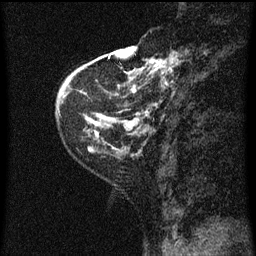
Breast MRI (dynamic contrast-enhanced), one sagittal slice. Slice 15 of 60 in the series (ordered by position). Dynamic contrast-enhanced series, image 2 of 3 at this slice position (ordered by acquisition). 1.5 T. TE 4.2 ms, TR 8 ms. 2 mm slice thickness. 256 × 256 image matrix, field of view 180 × 180 mm. Female patient, age 48 years.
Structures marked on this image (semi-automatic segmentation, software-assisted and operator-edited):
- analysis volume of interest (the breast-tissue region the enhancement analysis was run in; not a lesion): box from (x=128, y=54) to (x=175, y=125) px
- tumour enhancement mask (voxels above the 70 % enhancement threshold inside the analysis volume of interest): (x=128, y=54)–(x=175, y=121)